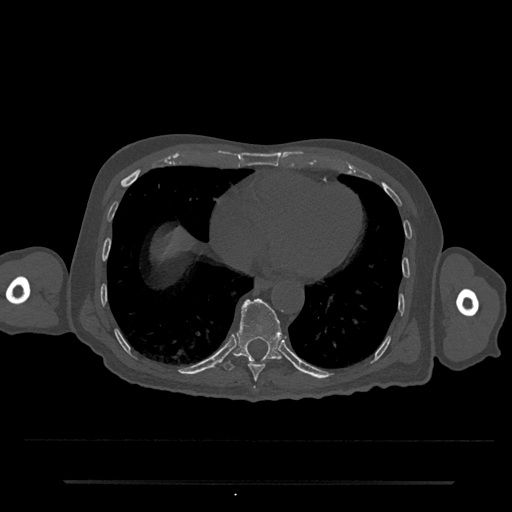
CT including the spine, one axial slice; position 336 of 797 along the scan axis; 120 kVp; bone window (W 1800 / L 400 HU); 0.5 mm slice thickness; 512 × 512 image matrix, field of view 427 × 427 mm. Male patient, age 74 years. Case-level facts recorded for this patient, not image findings: primary cancer: prostate.
Structures marked on this image (semi-automatic segmentation, software-assisted and operator-edited):
- T10 vertebra: box from (x=223, y=298) to (x=282, y=371) px
- T9 vertebra: (x=248, y=362)–(x=266, y=382)